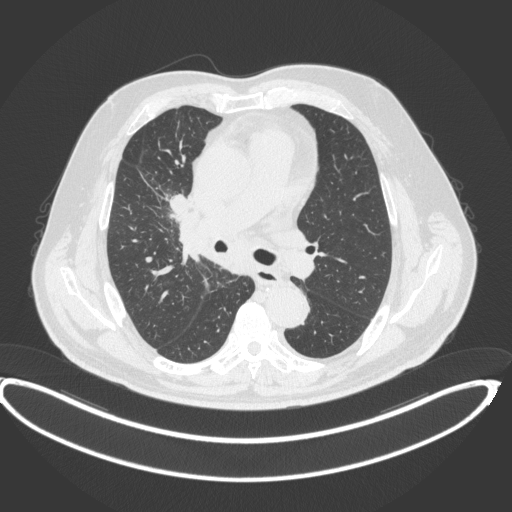
Chest CT, one axial slice. 120 kVp. Lung window (W 1500 / L -600 HU). 512 × 512 image matrix. Male patient, age 62 years. Case-level facts recorded for this patient, not image findings: clinical TNM (as recorded): T1c N3 M1c.
Structures marked on this image (bounding box drawn by a radiologist):
- lung tumour (recorded histology: adenocarcinoma): box from (x=170, y=190) to (x=191, y=212) px